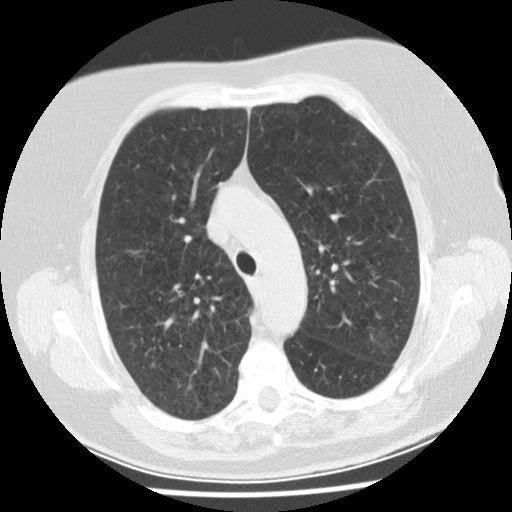
Chest CT (low-dose screening protocol), one axial image. First (baseline) screen. Lung window (W 1500 / L -600 HU). 120 kVp. Slice 115 of 149 in the series. Female participant, aged 74 years at enrolment.
Lesion marked by an expert reader, bounding box [x1, y1, x2, y2] px = [334, 312, 409, 370]. The screening reader recorded 2 non-calcified nodules or masses ≥4 mm on this exam (left upper lobe, left lower lobe); which of them this box marks is not recorded. Official screen result: positive, change unspecified: nodule(s) >= 4 mm or enlarging nodule(s), mass(es), or other non-specific abnormalities suspicious for lung cancer. Participant outcome: lung cancer diagnosed 532 days after this screen — bronchiolo-alveolar adenocarcinoma, NOS, left upper lobe, stage IA (AJCC 6th edition), 20 mm at pathology.